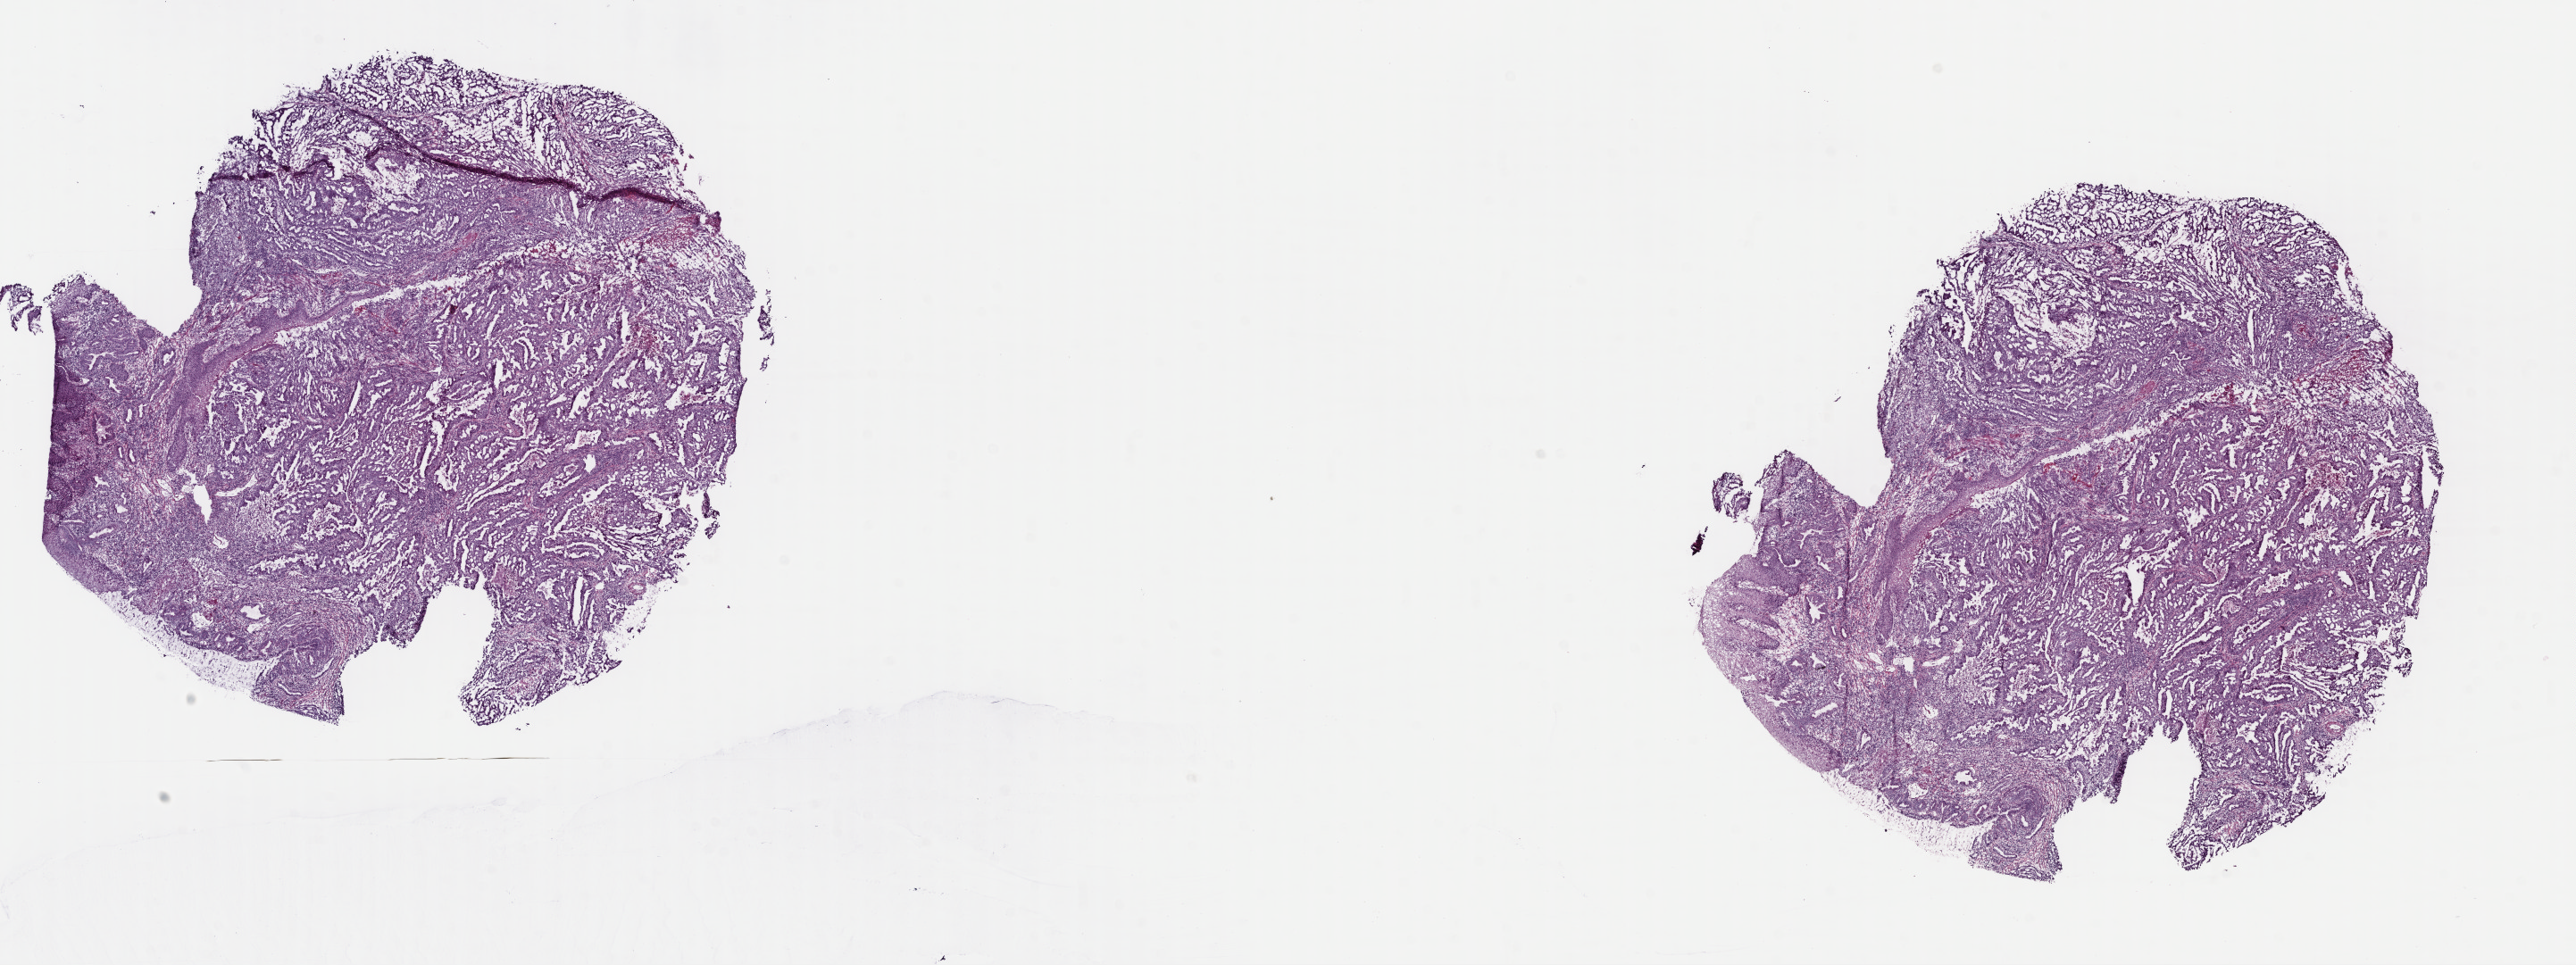
Hematoxylin and eosin (H&E) stained whole-slide image — shown as a low-resolution overview of the whole scanned area (about 22.7 x 8.5 mm, slide scanned at 40x), frozen section from the top of the tissue portion, sample: primary tumour, esophagus. Male, age 58 years at initial diagnosis. Histologic grade: G2 (moderately differentiated). Pathologist review of this section (percent, as recorded): tumour cells 90%, tumour nuclei 90%, normal cells 0%, stromal cells 10%, necrosis 0%. Inflammatory infiltration, as recorded: lymphocyte infiltration 40%, monocyte infiltration 20%, neutrophil infiltration 20%.
AJCC pathologic stage: IIA (7th edition). Pathologic diagnosis: Adenocarcinoma, NOS (lower third of esophagus). Lymph nodes positive (case pathology): 0 of 16 examined. TNM: T3 N0 M0.